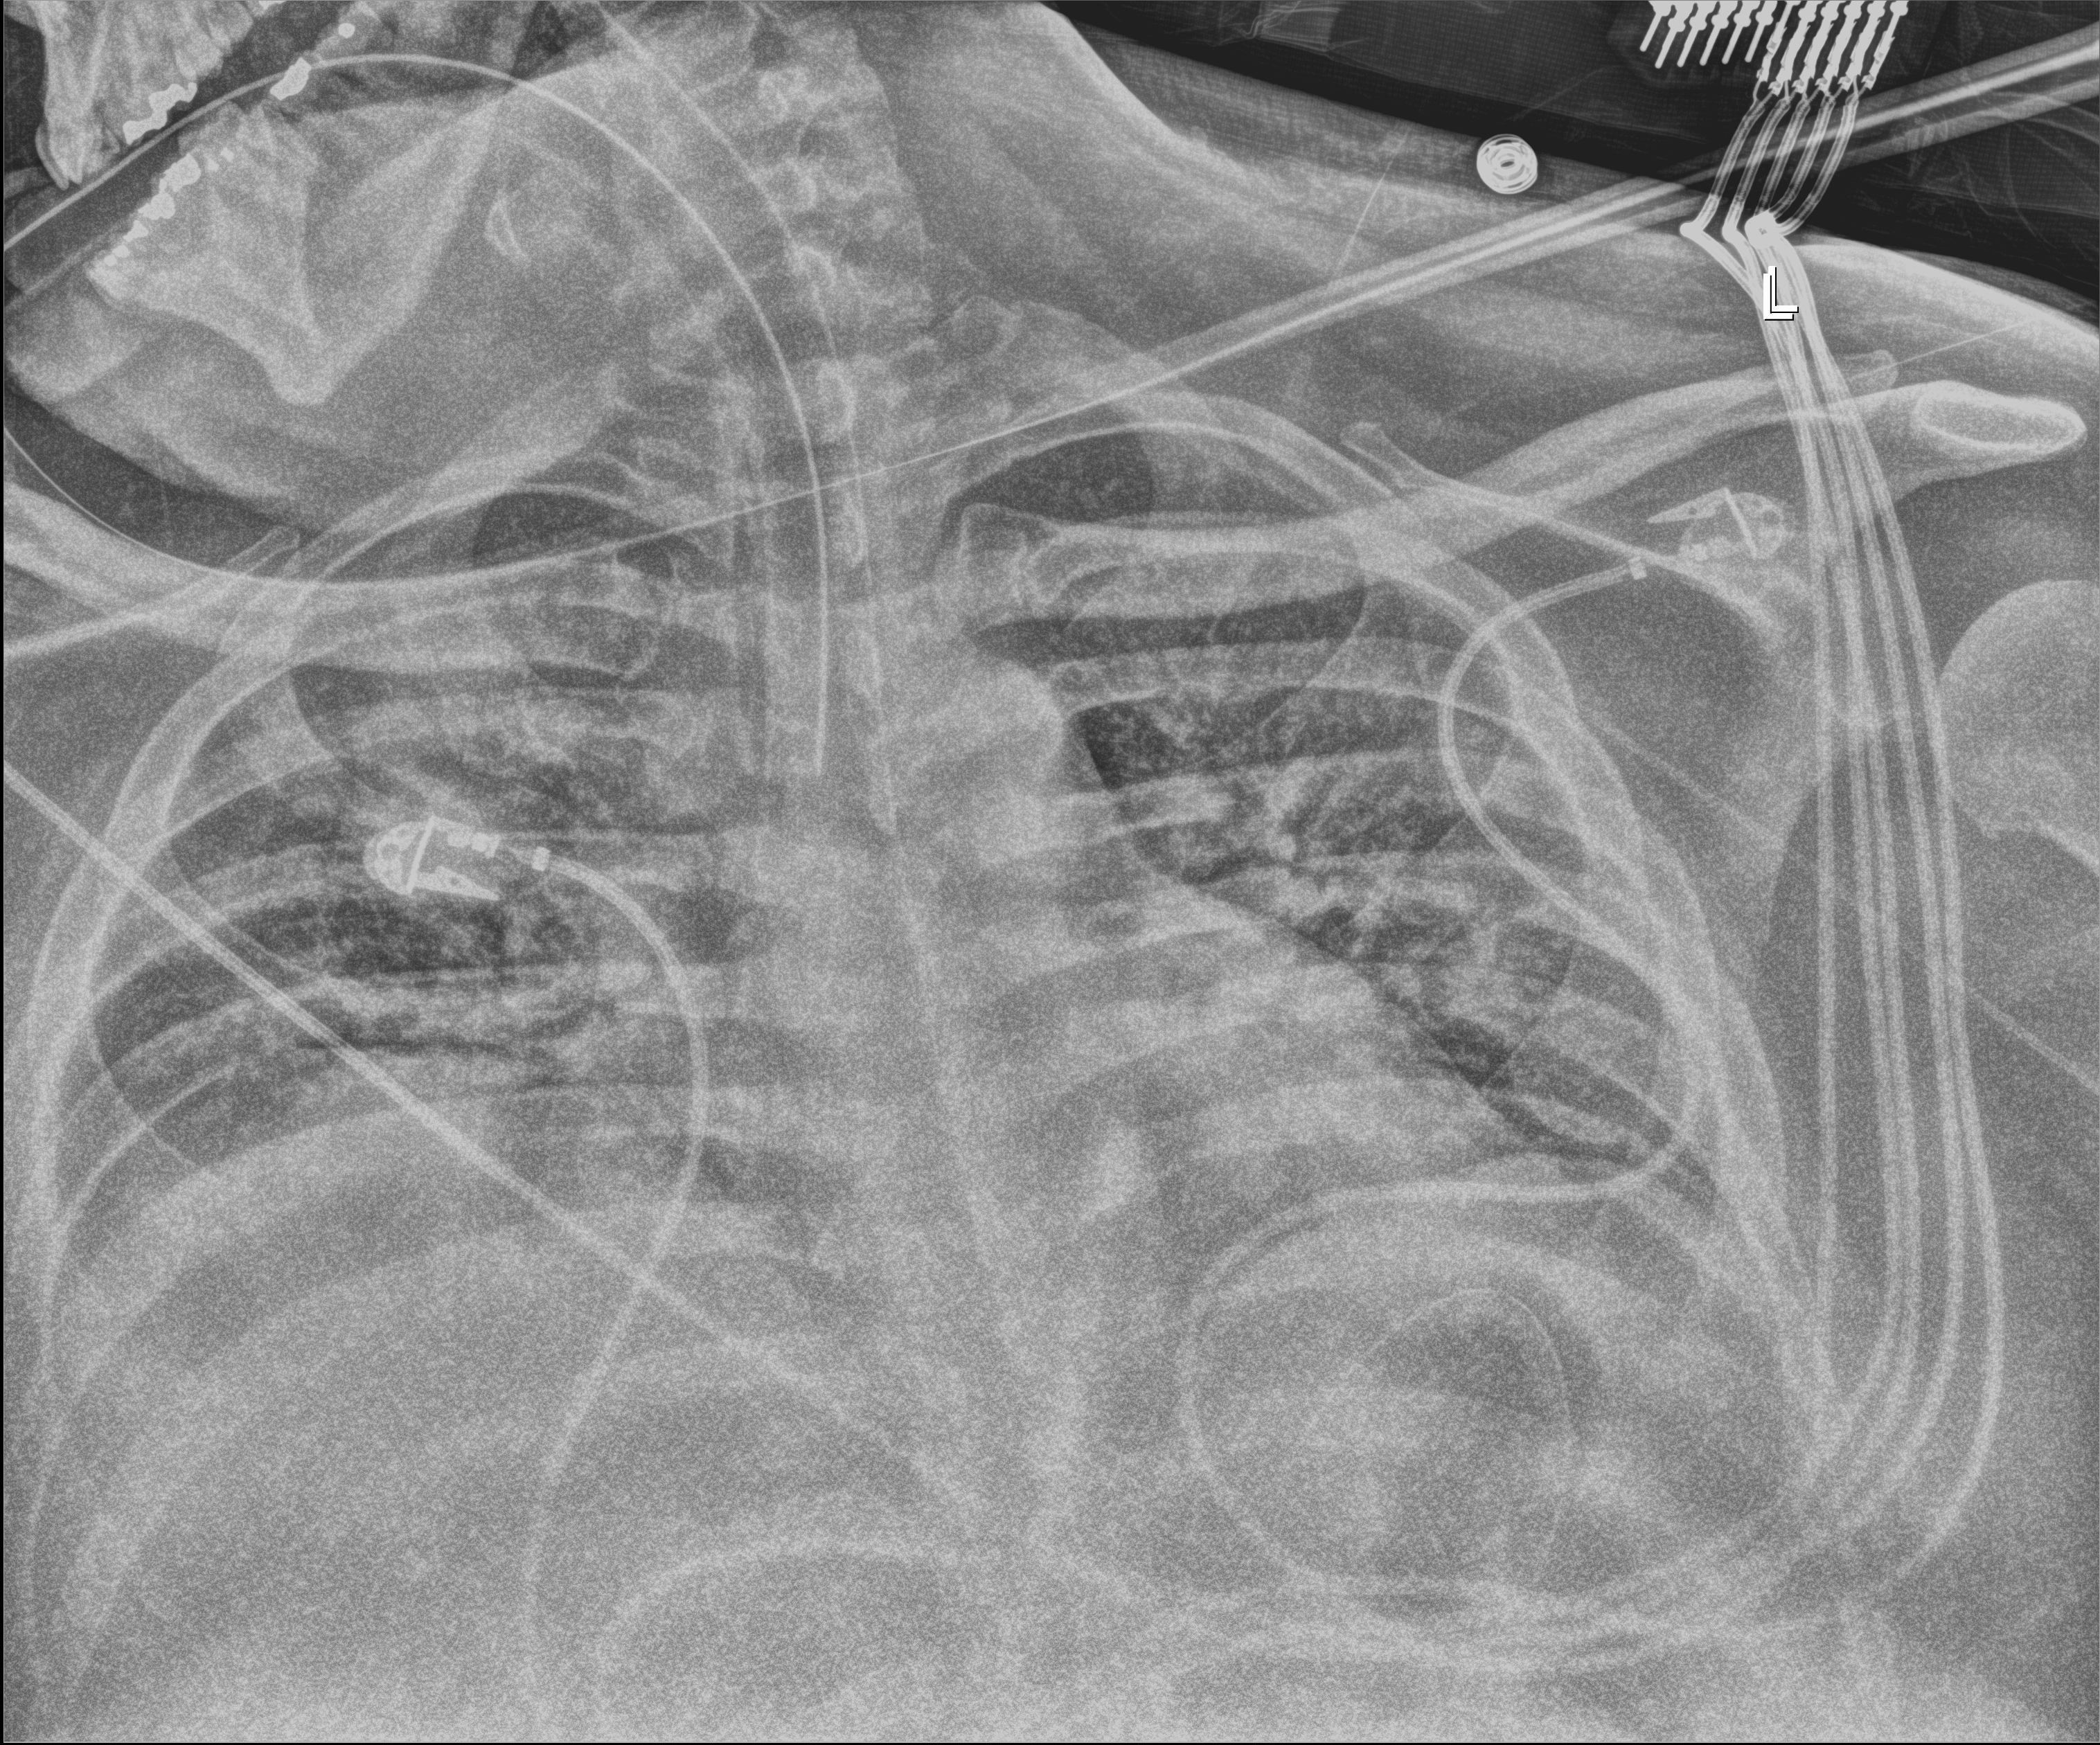
Chest X-ray (portable), anteroposterior (AP) projection. Male patient hospitalised with COVID-19, age 18–59 years.
Admission-level facts for this patient (not findings on this image; timing relative to this image not recorded):
- mechanically ventilated during this hospital stay: yes
- hypertension (admission record): no
- admitted to intensive care during this hospital stay: yes